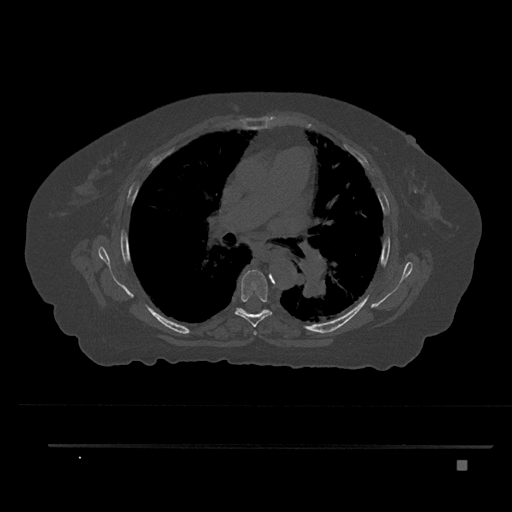
CT including the spine, one axial slice; slice 525 of 797 in the series (ordered by position); reconstruction kernel Br40s/3; 120 kVp; bone window (W 1800 / L 400 HU); 512 × 512 image matrix, field of view 437 × 437 mm. Patient: female, 76 years. From the clinical record (not read from this slice): primary cancer: lung; vertebrae with lytic lesions (as recorded): T11, L3.
Annotated regions visible in this slice (semi-automatically segmented with operator editing):
- T5 vertebra: box from (x=253, y=331) to (x=257, y=335) px
- T6 vertebra: (x=235, y=269)–(x=272, y=327)
- T7 vertebra: (x=237, y=308)–(x=268, y=312)